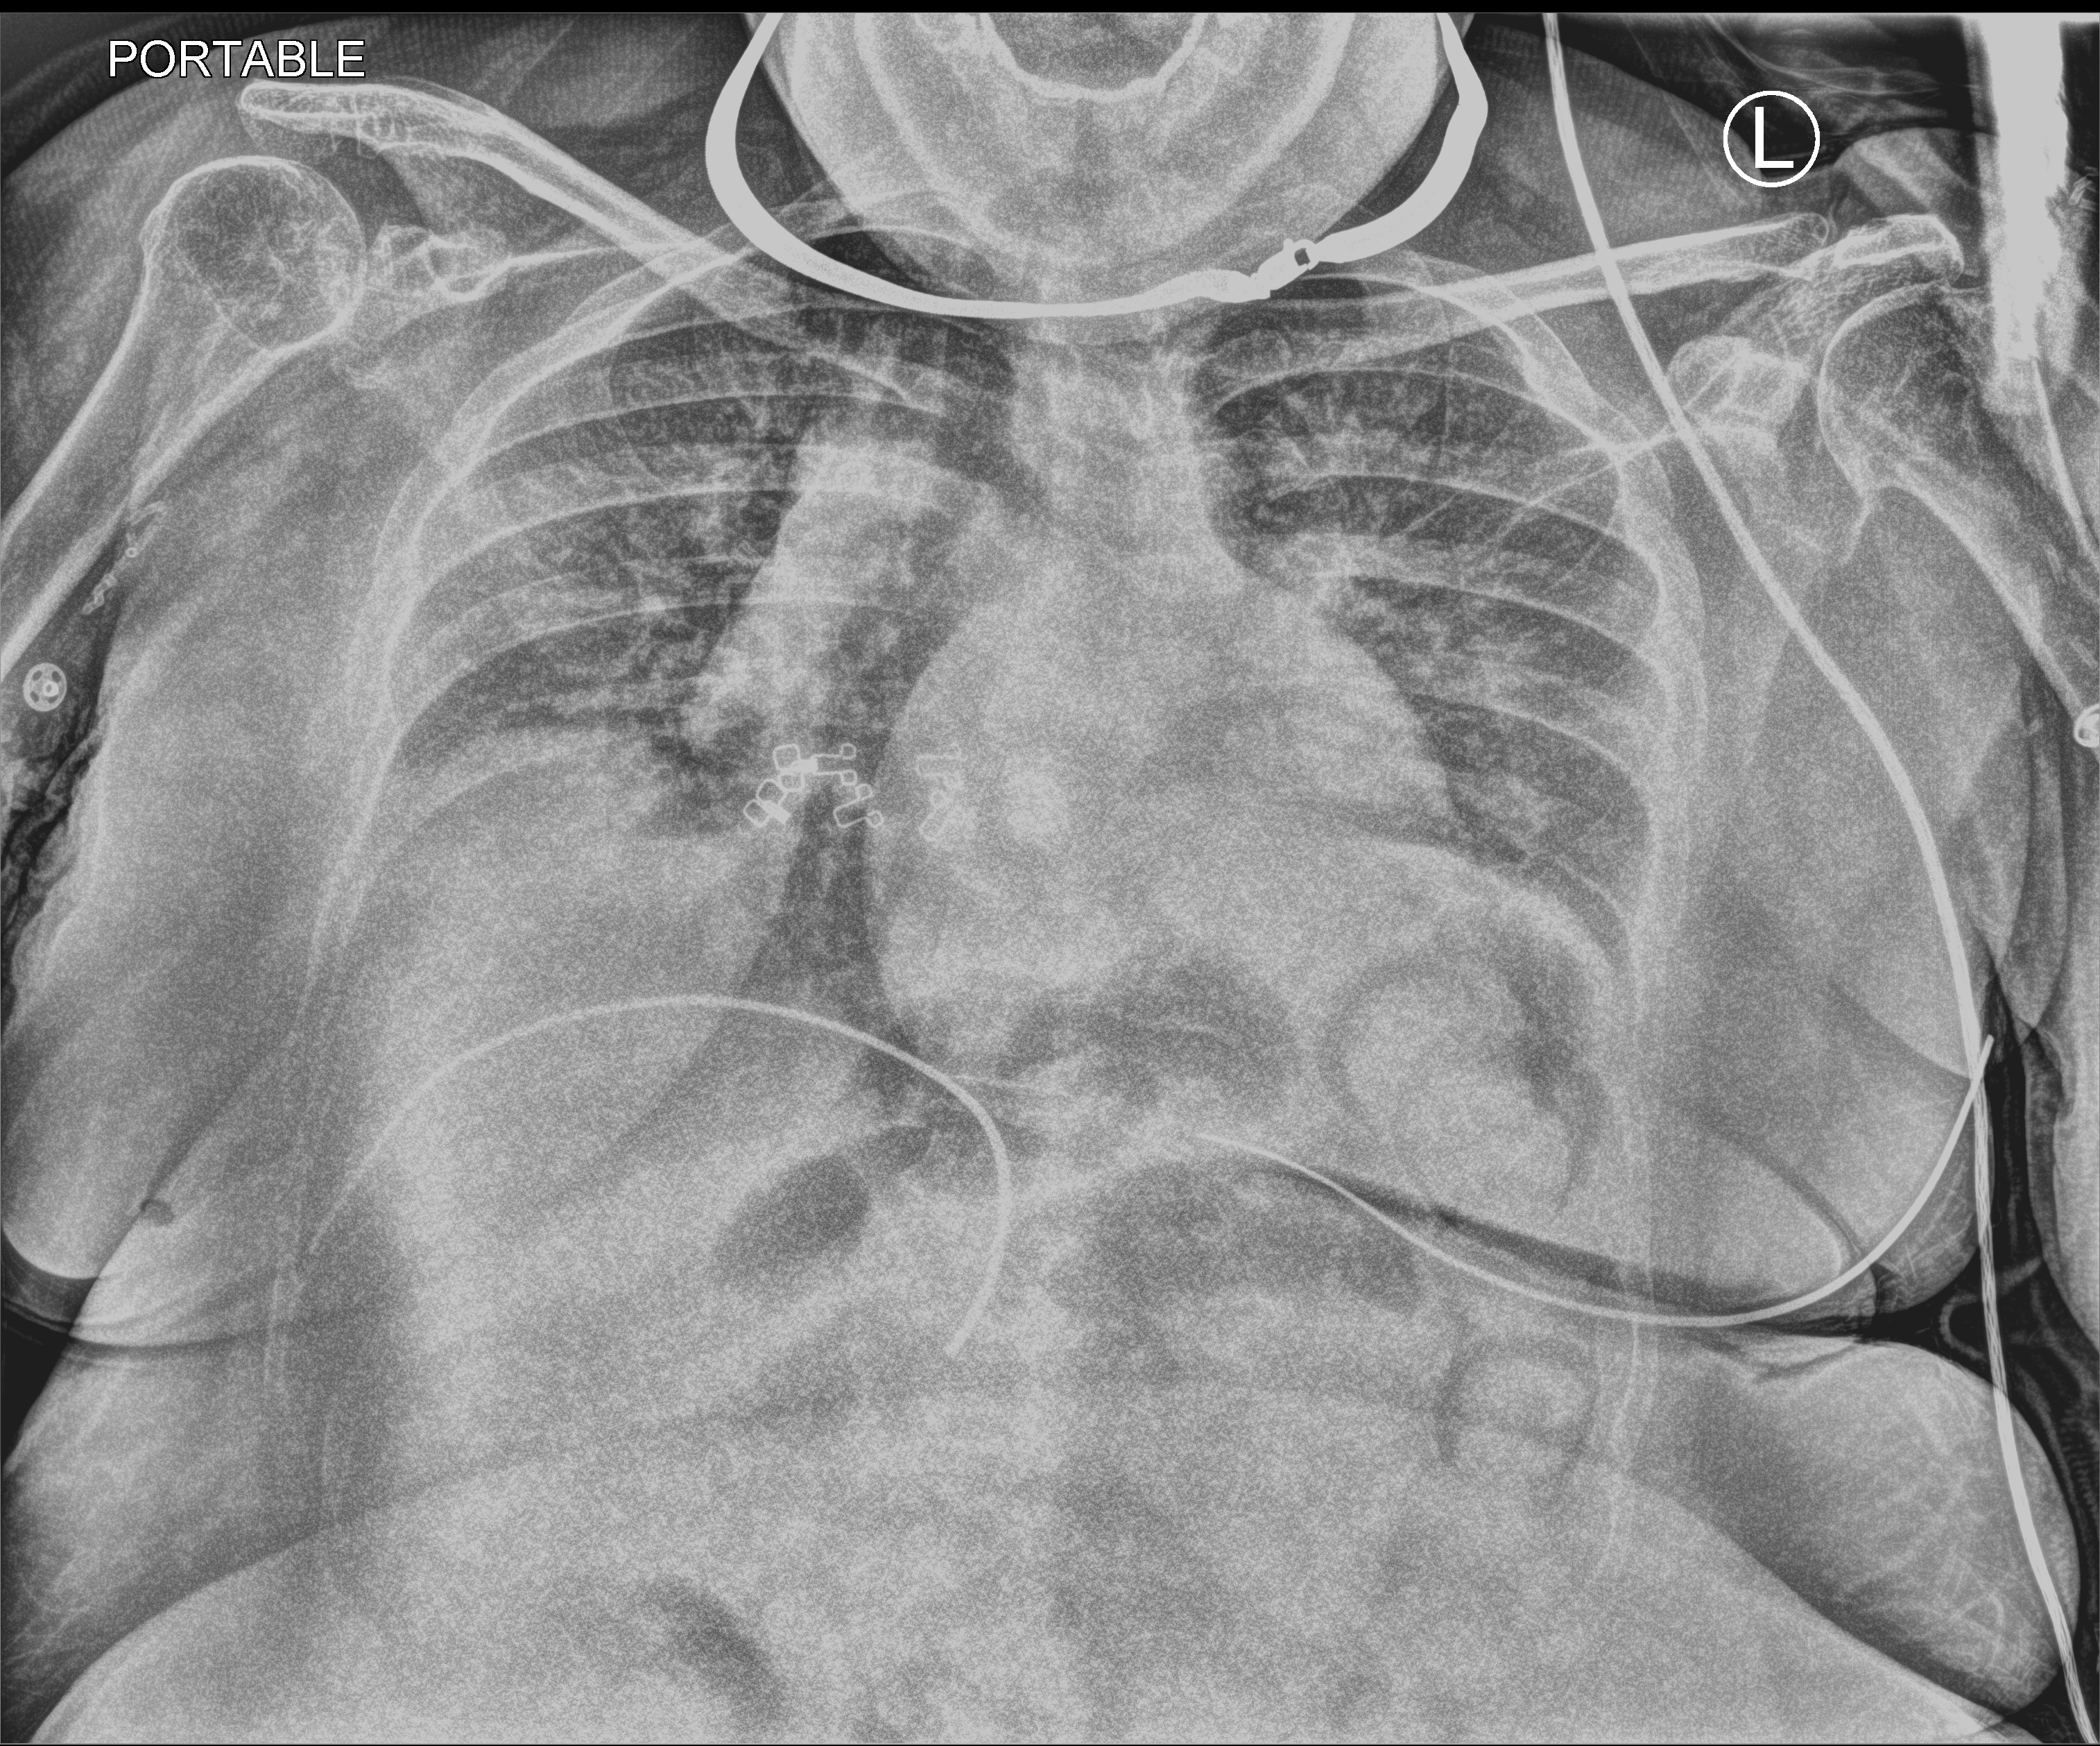
Bedside chest radiograph (computed radiography); anteroposterior (AP) projection. Female patient hospitalised with COVID-19, age 18–59 years.
Hospital-stay facts (about this admission, not read from this image; timing relative to this image not recorded):
- COPD (admission record): no